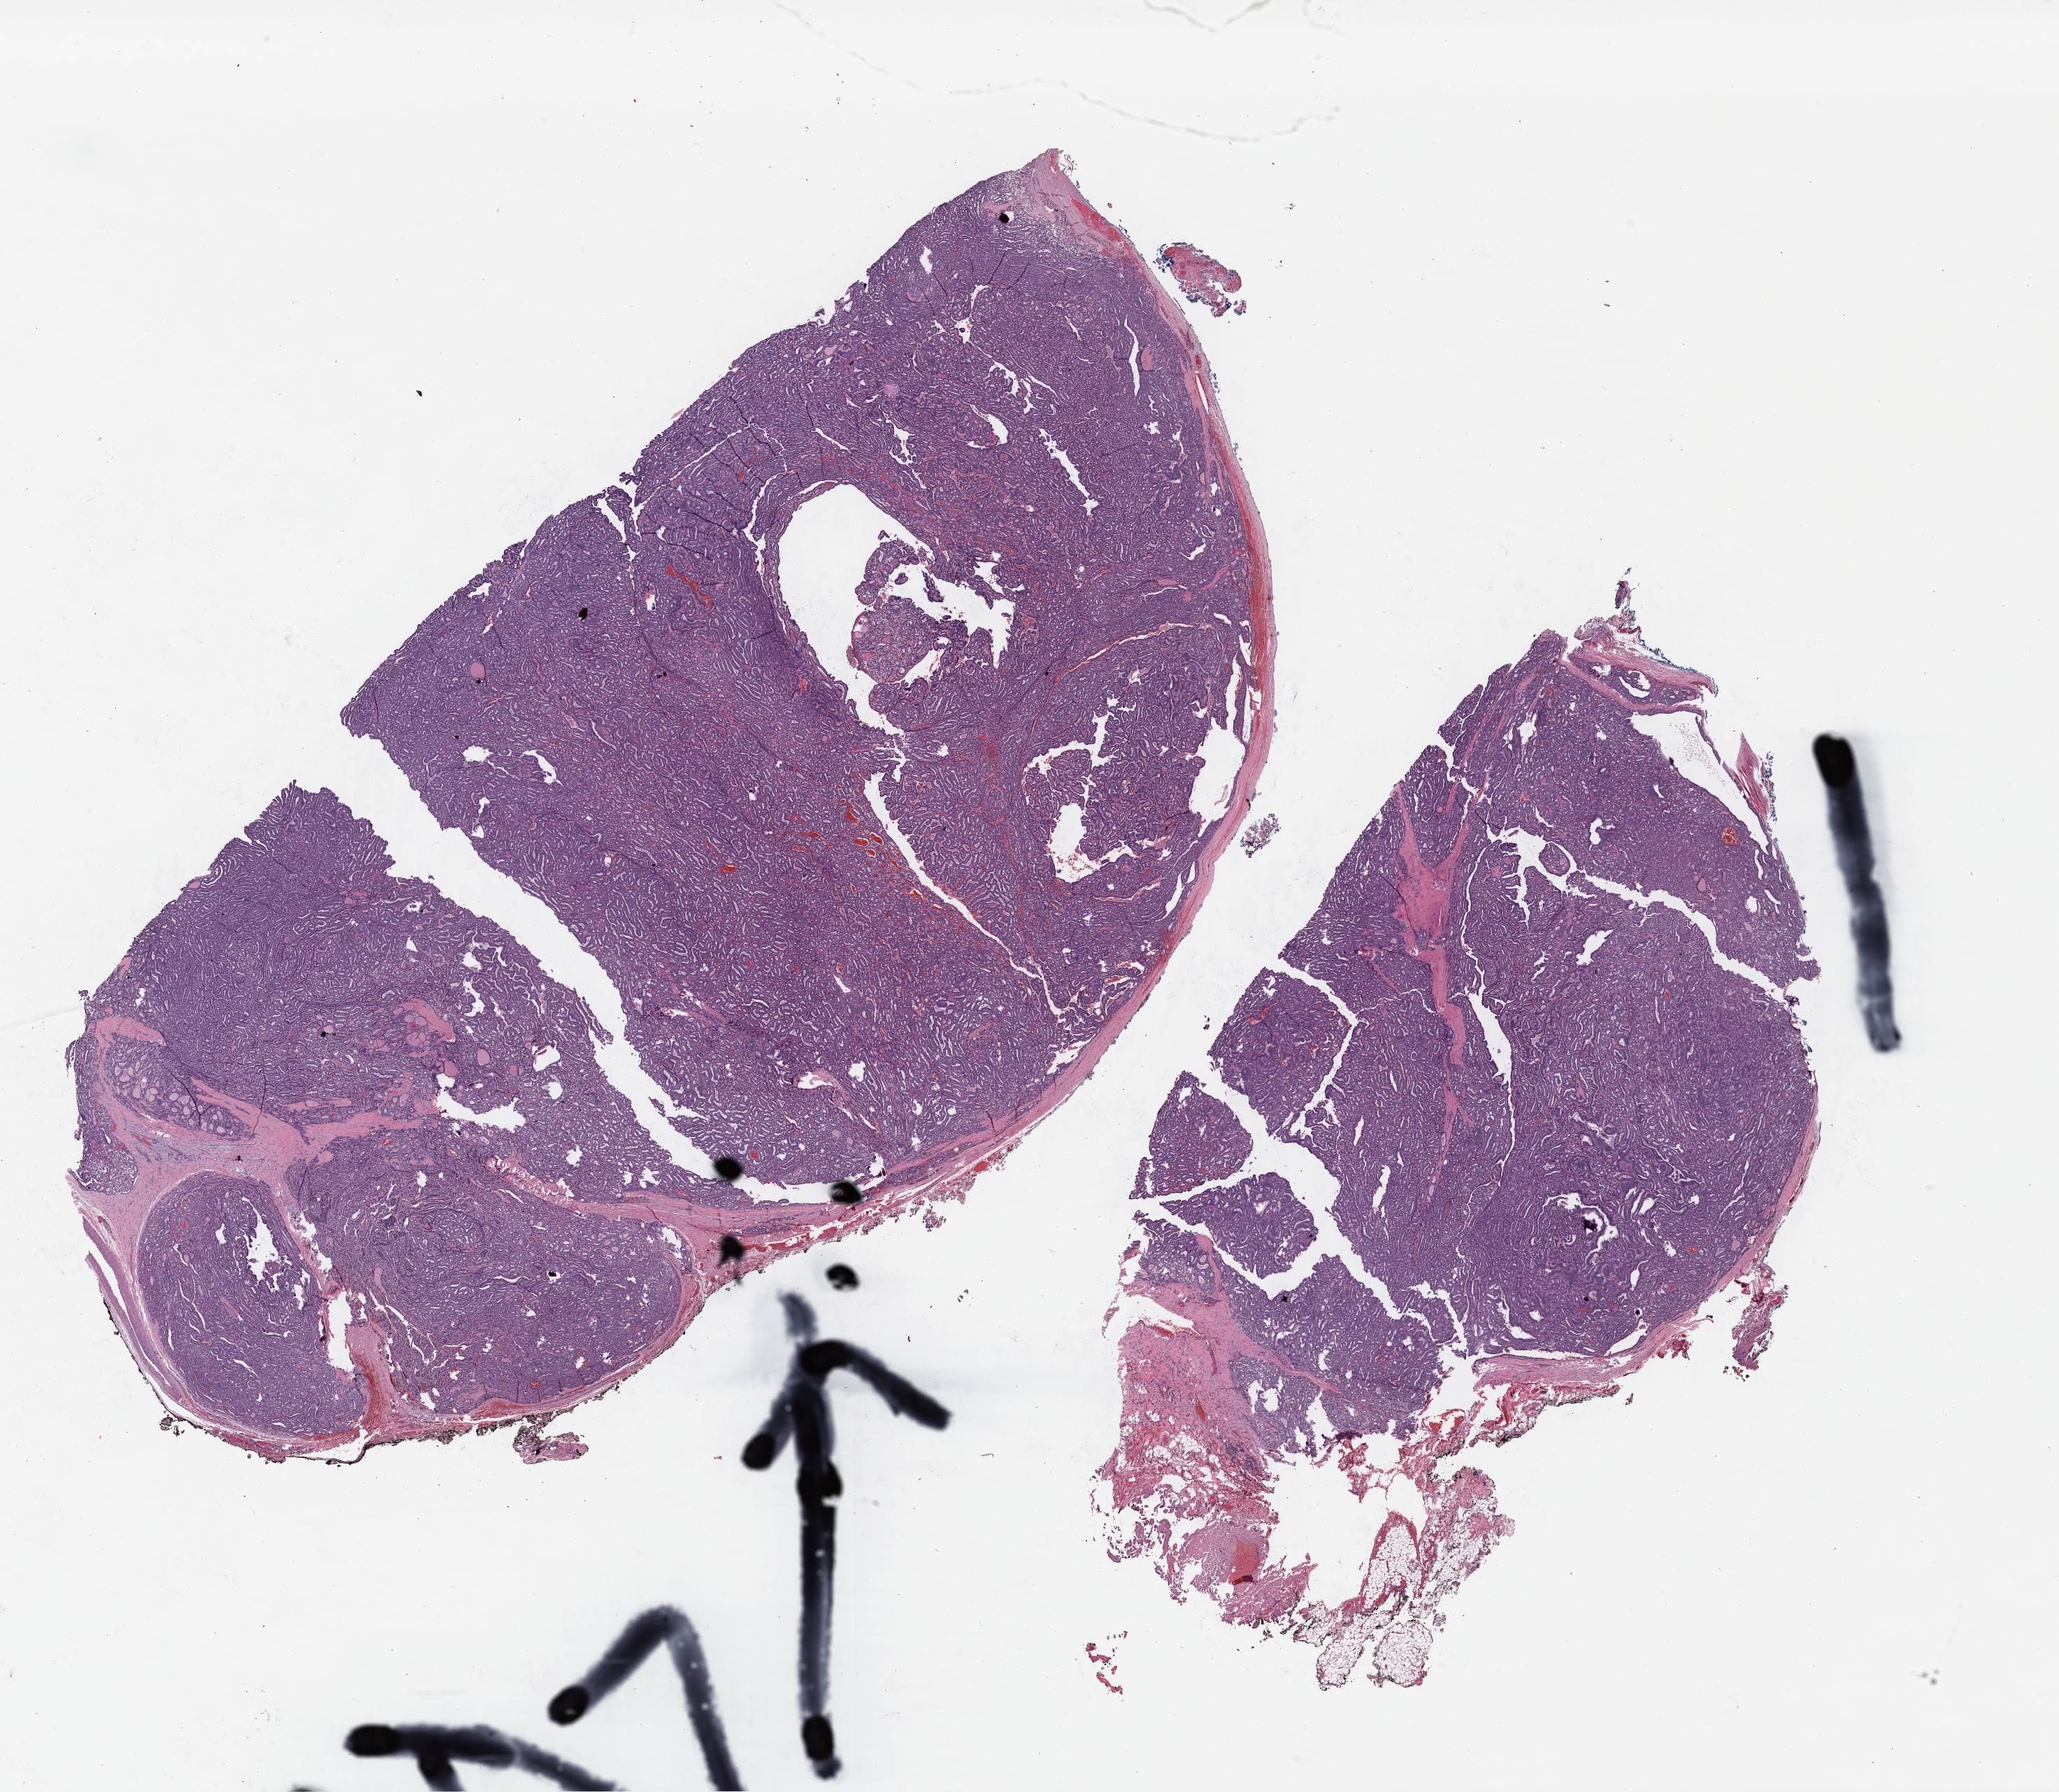
H&E whole-slide image — shown as a low-resolution overview of the whole scanned area (about 23.1 x 20.1 mm, slide scanned at 40x); FFPE section; sample: primary tumour, thyroid. Female, age 20 years at initial diagnosis.
Pathologic diagnosis: Papillary adenocarcinoma, NOS (thyroid gland). AJCC pathologic stage: I (7th edition). Lymph nodes positive (case pathology): 0 of 2 examined.